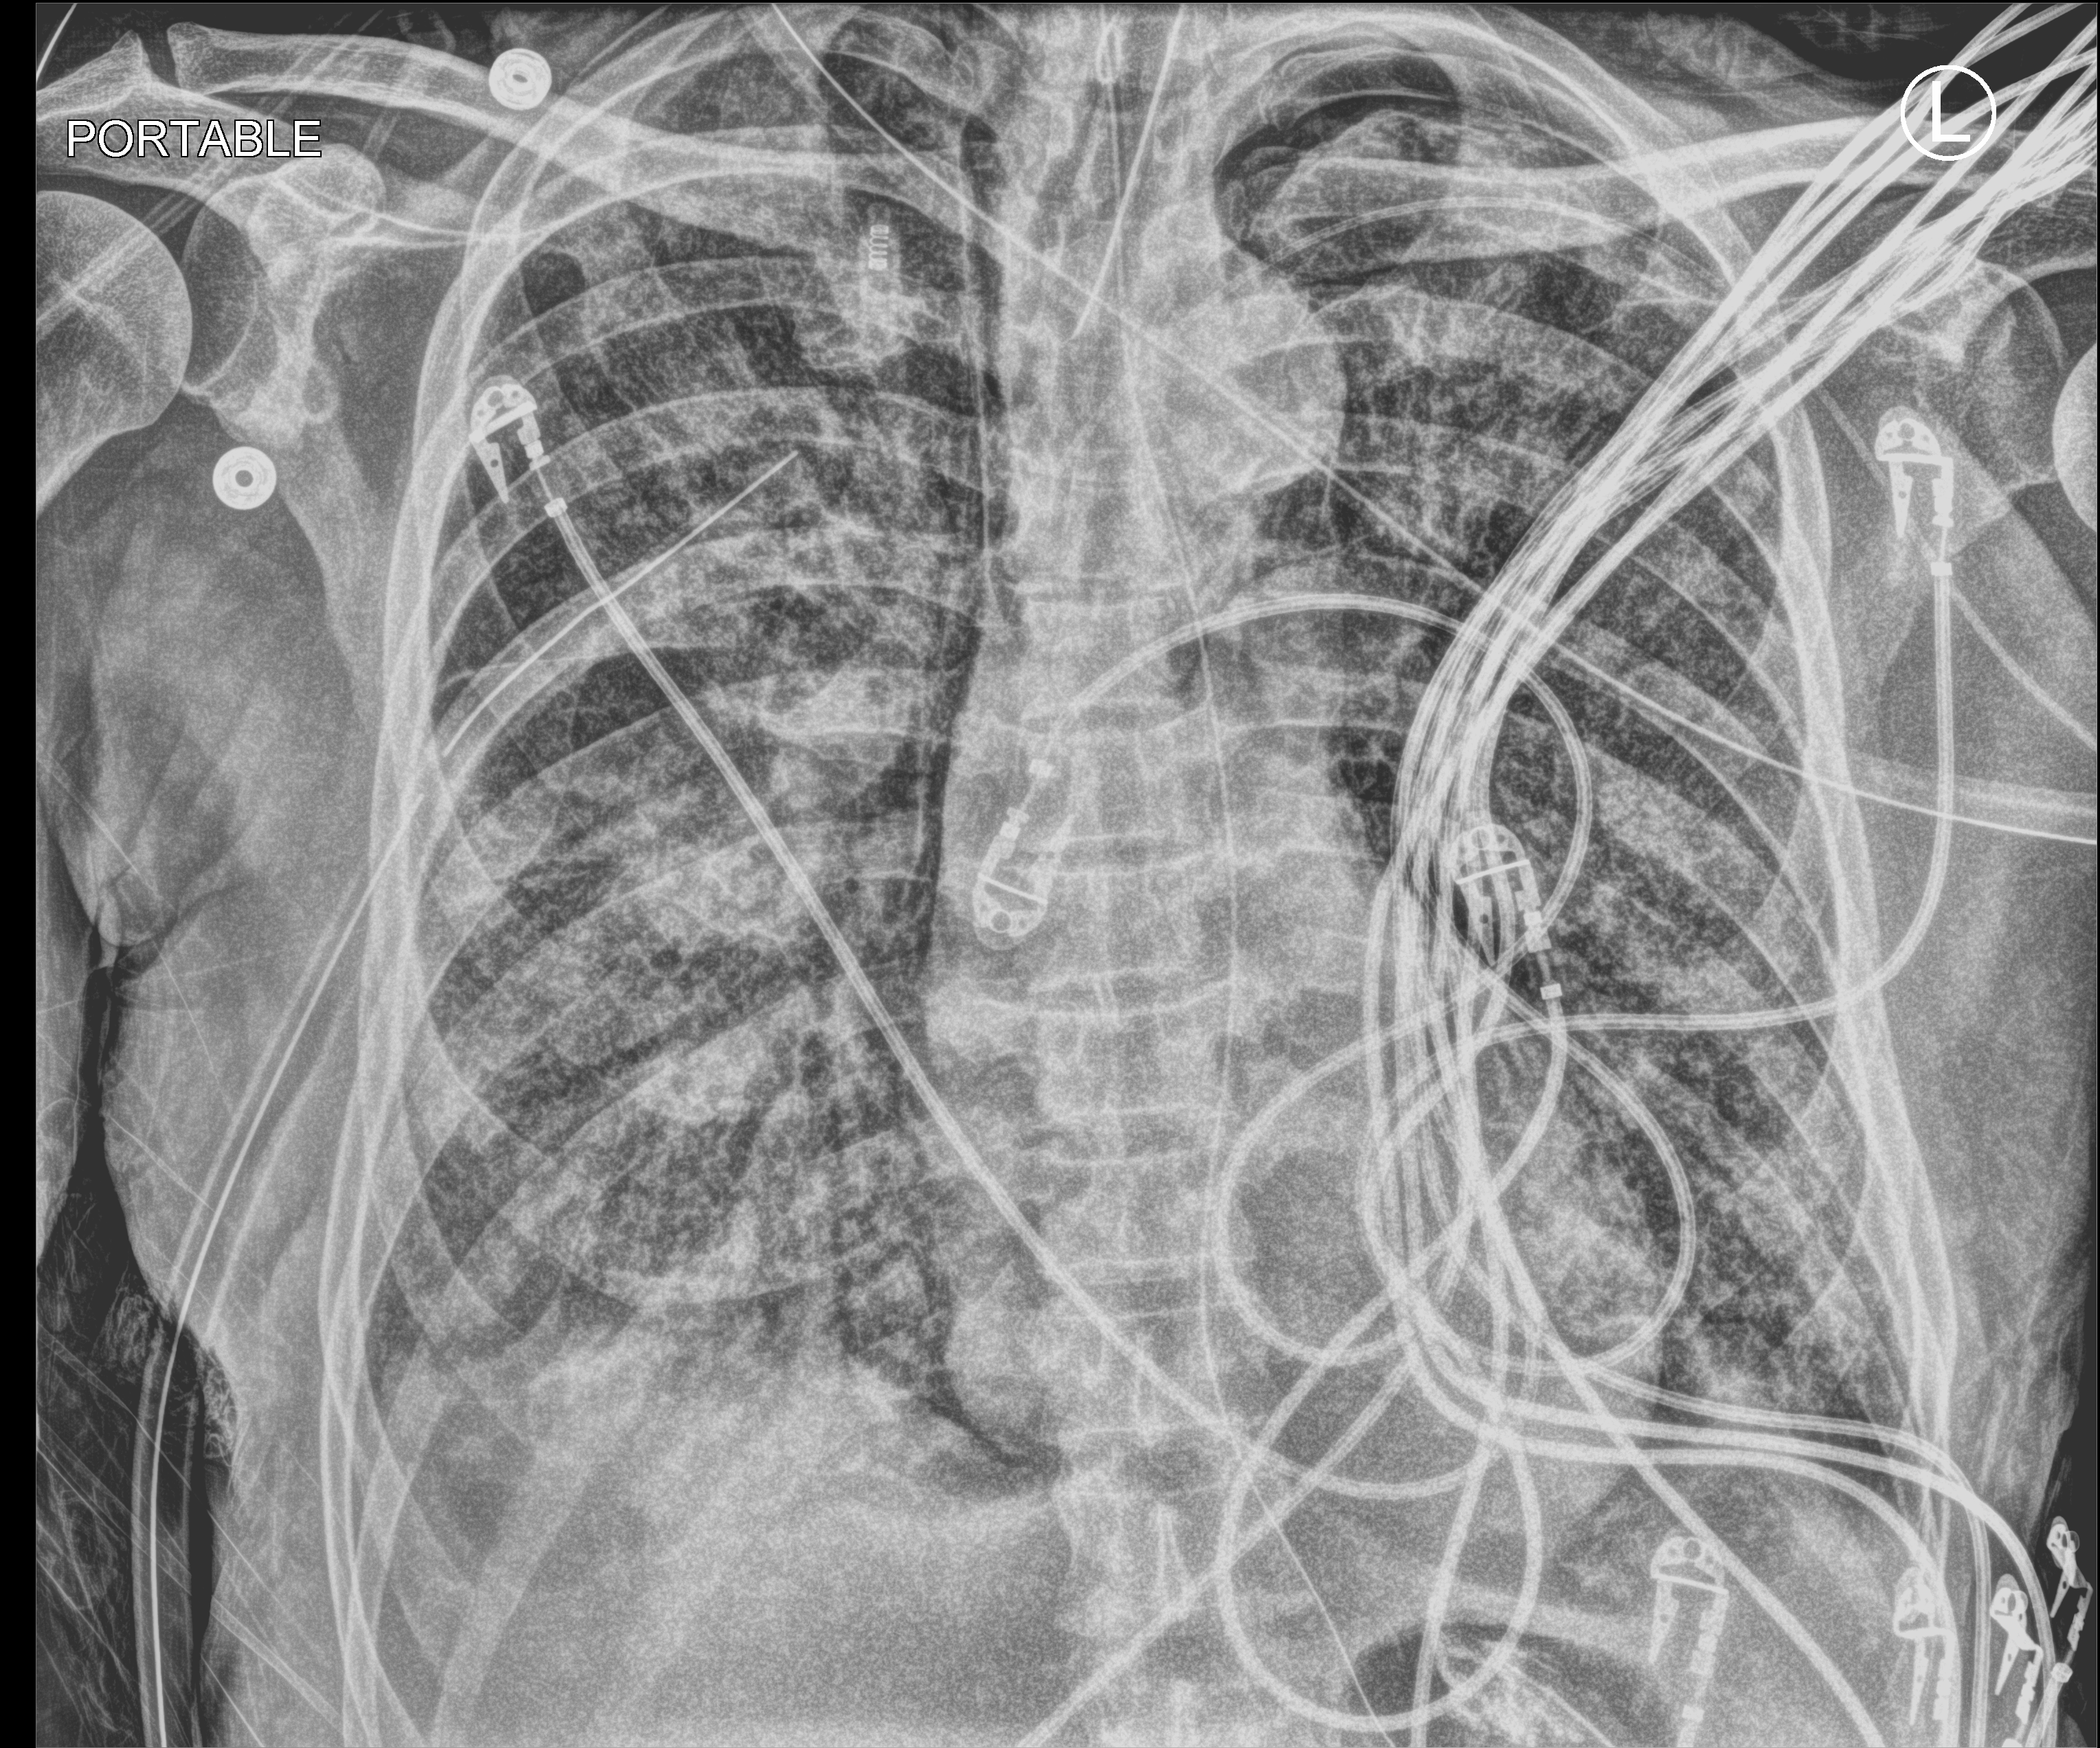
Bedside chest radiograph (computed radiography); anteroposterior (AP) projection. Patient hospitalised with COVID-19; male, aged 60–74 years.
Admission-level facts for this patient (not findings on this image; timing relative to this image not recorded):
- length of hospital stay: 31 days